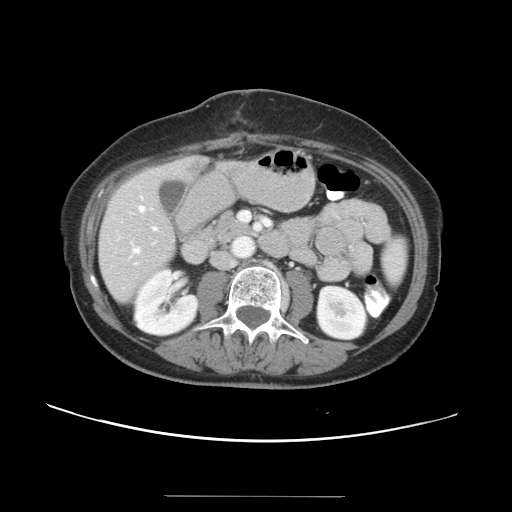
Contrast-enhanced abdominal CT, one axial slice. Slice 11 of 34 in the series (ordered by position). 120 kVp. Intravenous contrast given. Soft-tissue window (W 400 / L 40 HU). 5 mm slice thickness. 512 × 512 image matrix, field of view 382 × 382 mm. Female patient, age 69 years. From the clinical record (not read from this slice): diagnosis: colorectal cancer liver metastases, imaged before liver resection; multiple liver metastases: yes; largest metastasis: 1.4 cm; chemotherapy before resection: no.
Structures marked on this image (manually delineated by an expert):
- hepatic veins: bounding box (x1, y1, x2, y2) in pixels: (133, 205, 152, 254)
- liver: (99, 157, 240, 302)
- planned liver remnant (the part of the liver to remain after resection): (99, 157, 242, 302)
- portal vein (with intrahepatic branches): (135, 212, 270, 251)